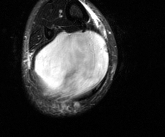
MRI of an extremity soft-tissue mass, one axial slice. Position 45 of 81 along the scan axis. T2-weighted fat-saturated. MR volume resampled by the dataset authors to the PET/CT grid (not the native acquisition matrix). 3.27 mm slice thickness. 165 × 137 image matrix. Male patient. From the clinical record (not read from this slice): histological type: liposarcoma - round cell; grade: high; site of the primary tumour: right calf.
Structures marked on this image (expert contour drawn on MRI and transferred to this co-registered scan by the dataset authors):
- gross tumour volume (mass): bounding box <34,30,109,99> (left, top, right, bottom; pixels)